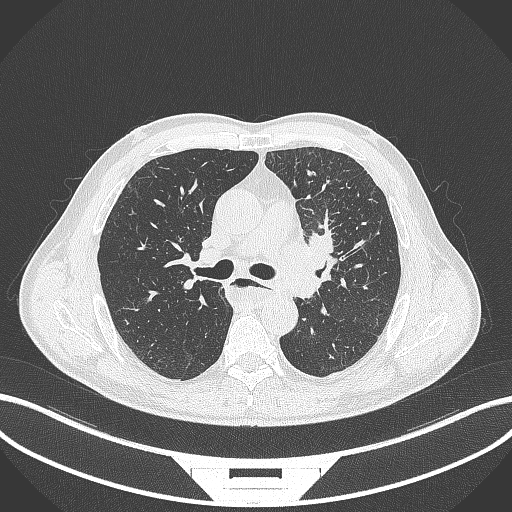
Chest CT, one axial slice; slice 235 of 411 in the series (ordered by position); reconstruction kernel B70f; 120 kVp; lung window (W 1500 / L -600 HU); 1 mm slice thickness; 512 × 512 image matrix. Male patient, age 57 years. From the clinical record (not read from this slice): clinical TNM (as recorded): T2a N1 M0.
Structures marked on this image (bounding box drawn by a radiologist):
- lung tumour (recorded histology: squamous cell carcinoma): bounding box (x1, y1, x2, y2) in pixels: (274, 225, 340, 307)